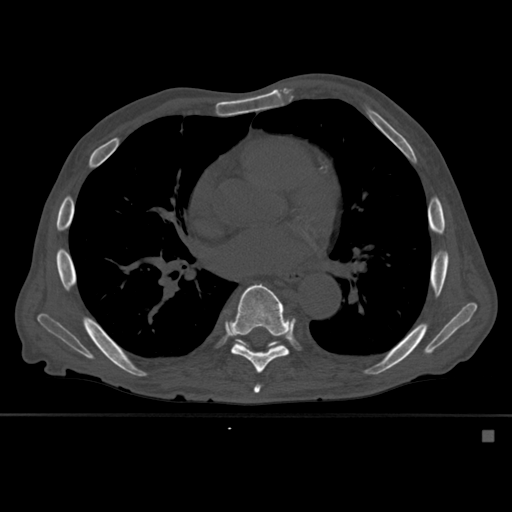
CT including the spine, one axial slice; position 349 of 527 along the scan axis; bone window (W 1800 / L 400 HU); 1.5 mm slice thickness; 512 × 512 image matrix. Male patient, age 78 years. Case-level facts recorded for this patient, not image findings: primary cancer: prostate.
Structures marked on this image (semi-automatic segmentation, software-assisted and operator-edited):
- T7 vertebra: bounding box (x1, y1, x2, y2) in pixels: (240, 298, 261, 394)
- T8 vertebra: (230, 283, 293, 374)
- T9 vertebra: (232, 339, 283, 350)